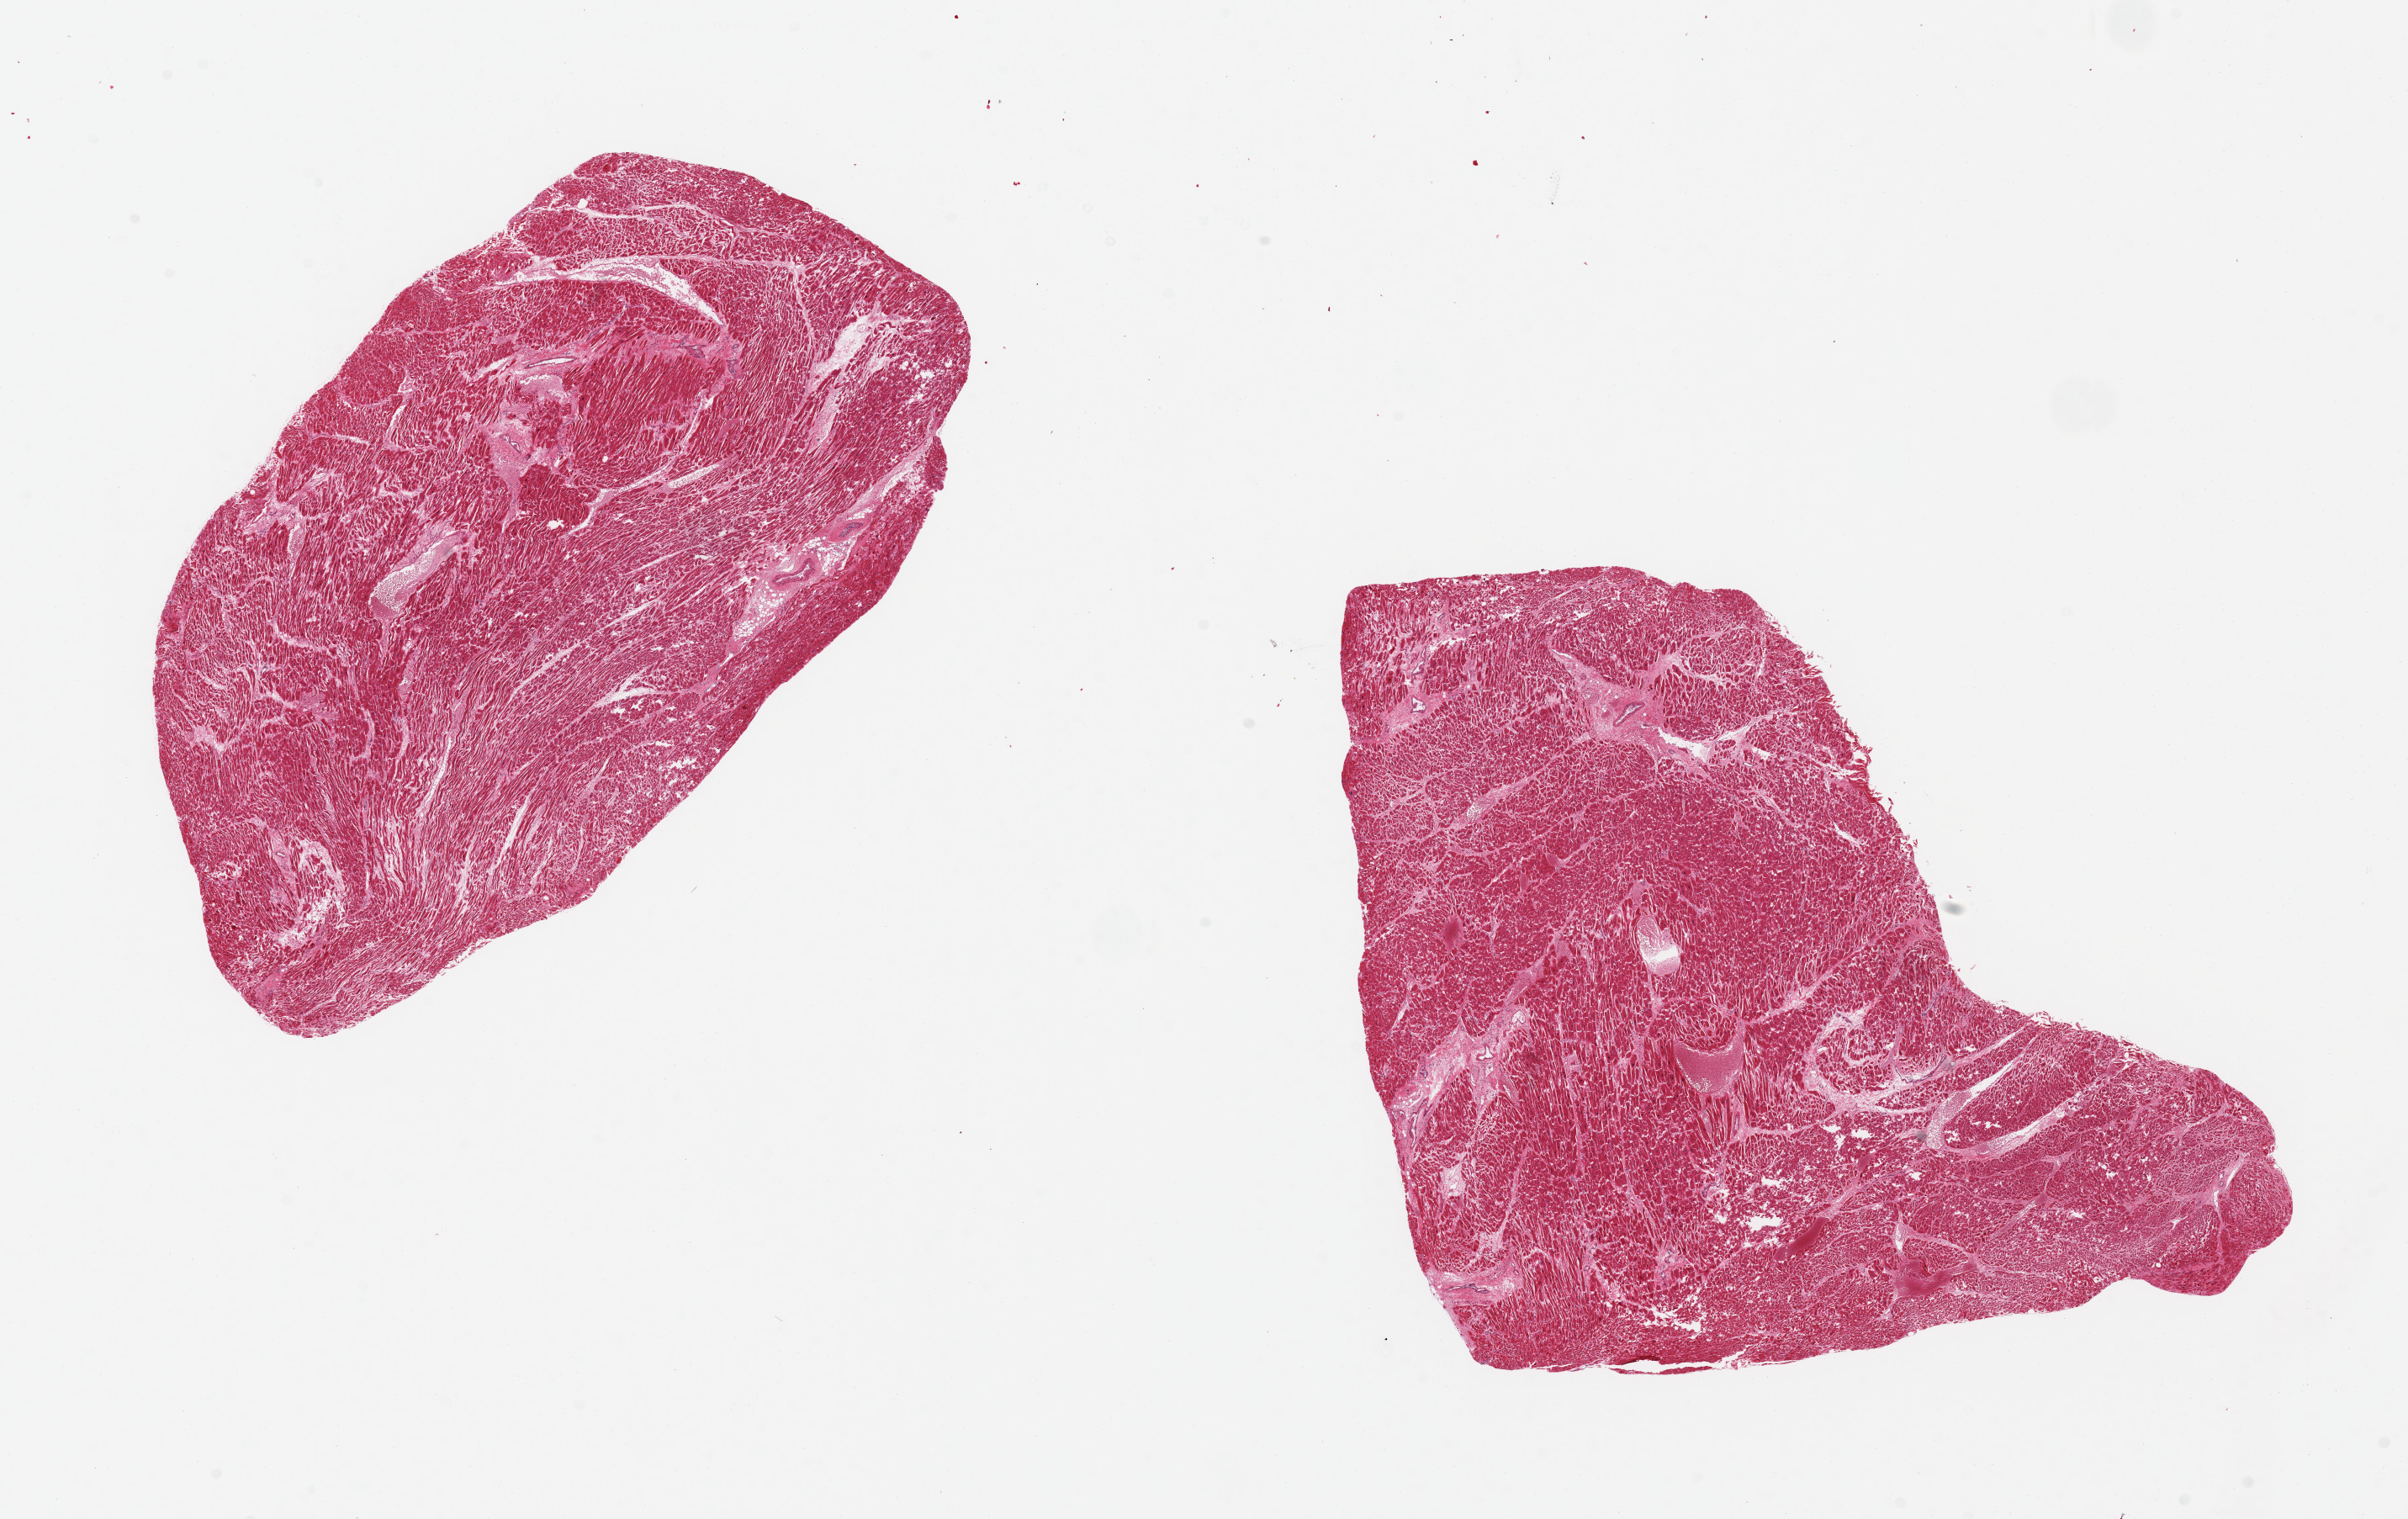
Whole-slide image, H&E stain, brightfield, a low-resolution overview of the entire scanned area, about 22.6 x 14.3 mm (acquisition: 20x scan). PAXgene-fixed paraffin-embedded (PFPE) section. Sampled site (target tissue): heart. Donor tissue sample. Donor sex: male.
* pathologist's review note for this sample: 2 pieces 9x4 & 7x7 mm; fiber fracture autolysis artifact